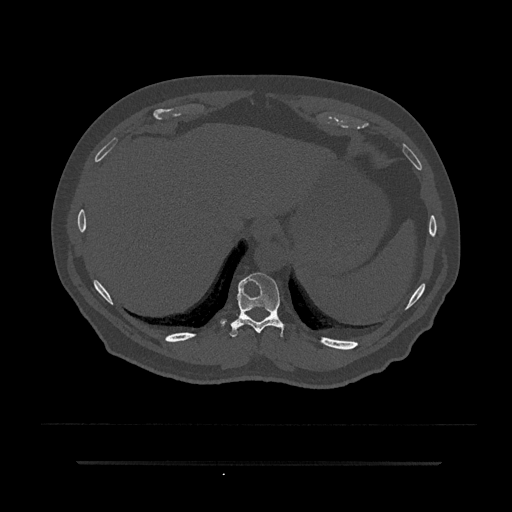
CT including the spine, one axial slice; reconstruction kernel Br40s/3; 120 kVp; bone window (W 1800 / L 400 HU); 0.5 mm slice thickness; 512 × 512 image matrix, field of view 464 × 464 mm. Male patient, age 59 years. Case-level facts recorded for this patient, not image findings: primary cancer: bile ducts.
Outlined on this slice (semi-automatically segmented with operator editing):
- T10 vertebra: bounding box [x1, y1, x2, y2] px = [221, 273, 285, 337]